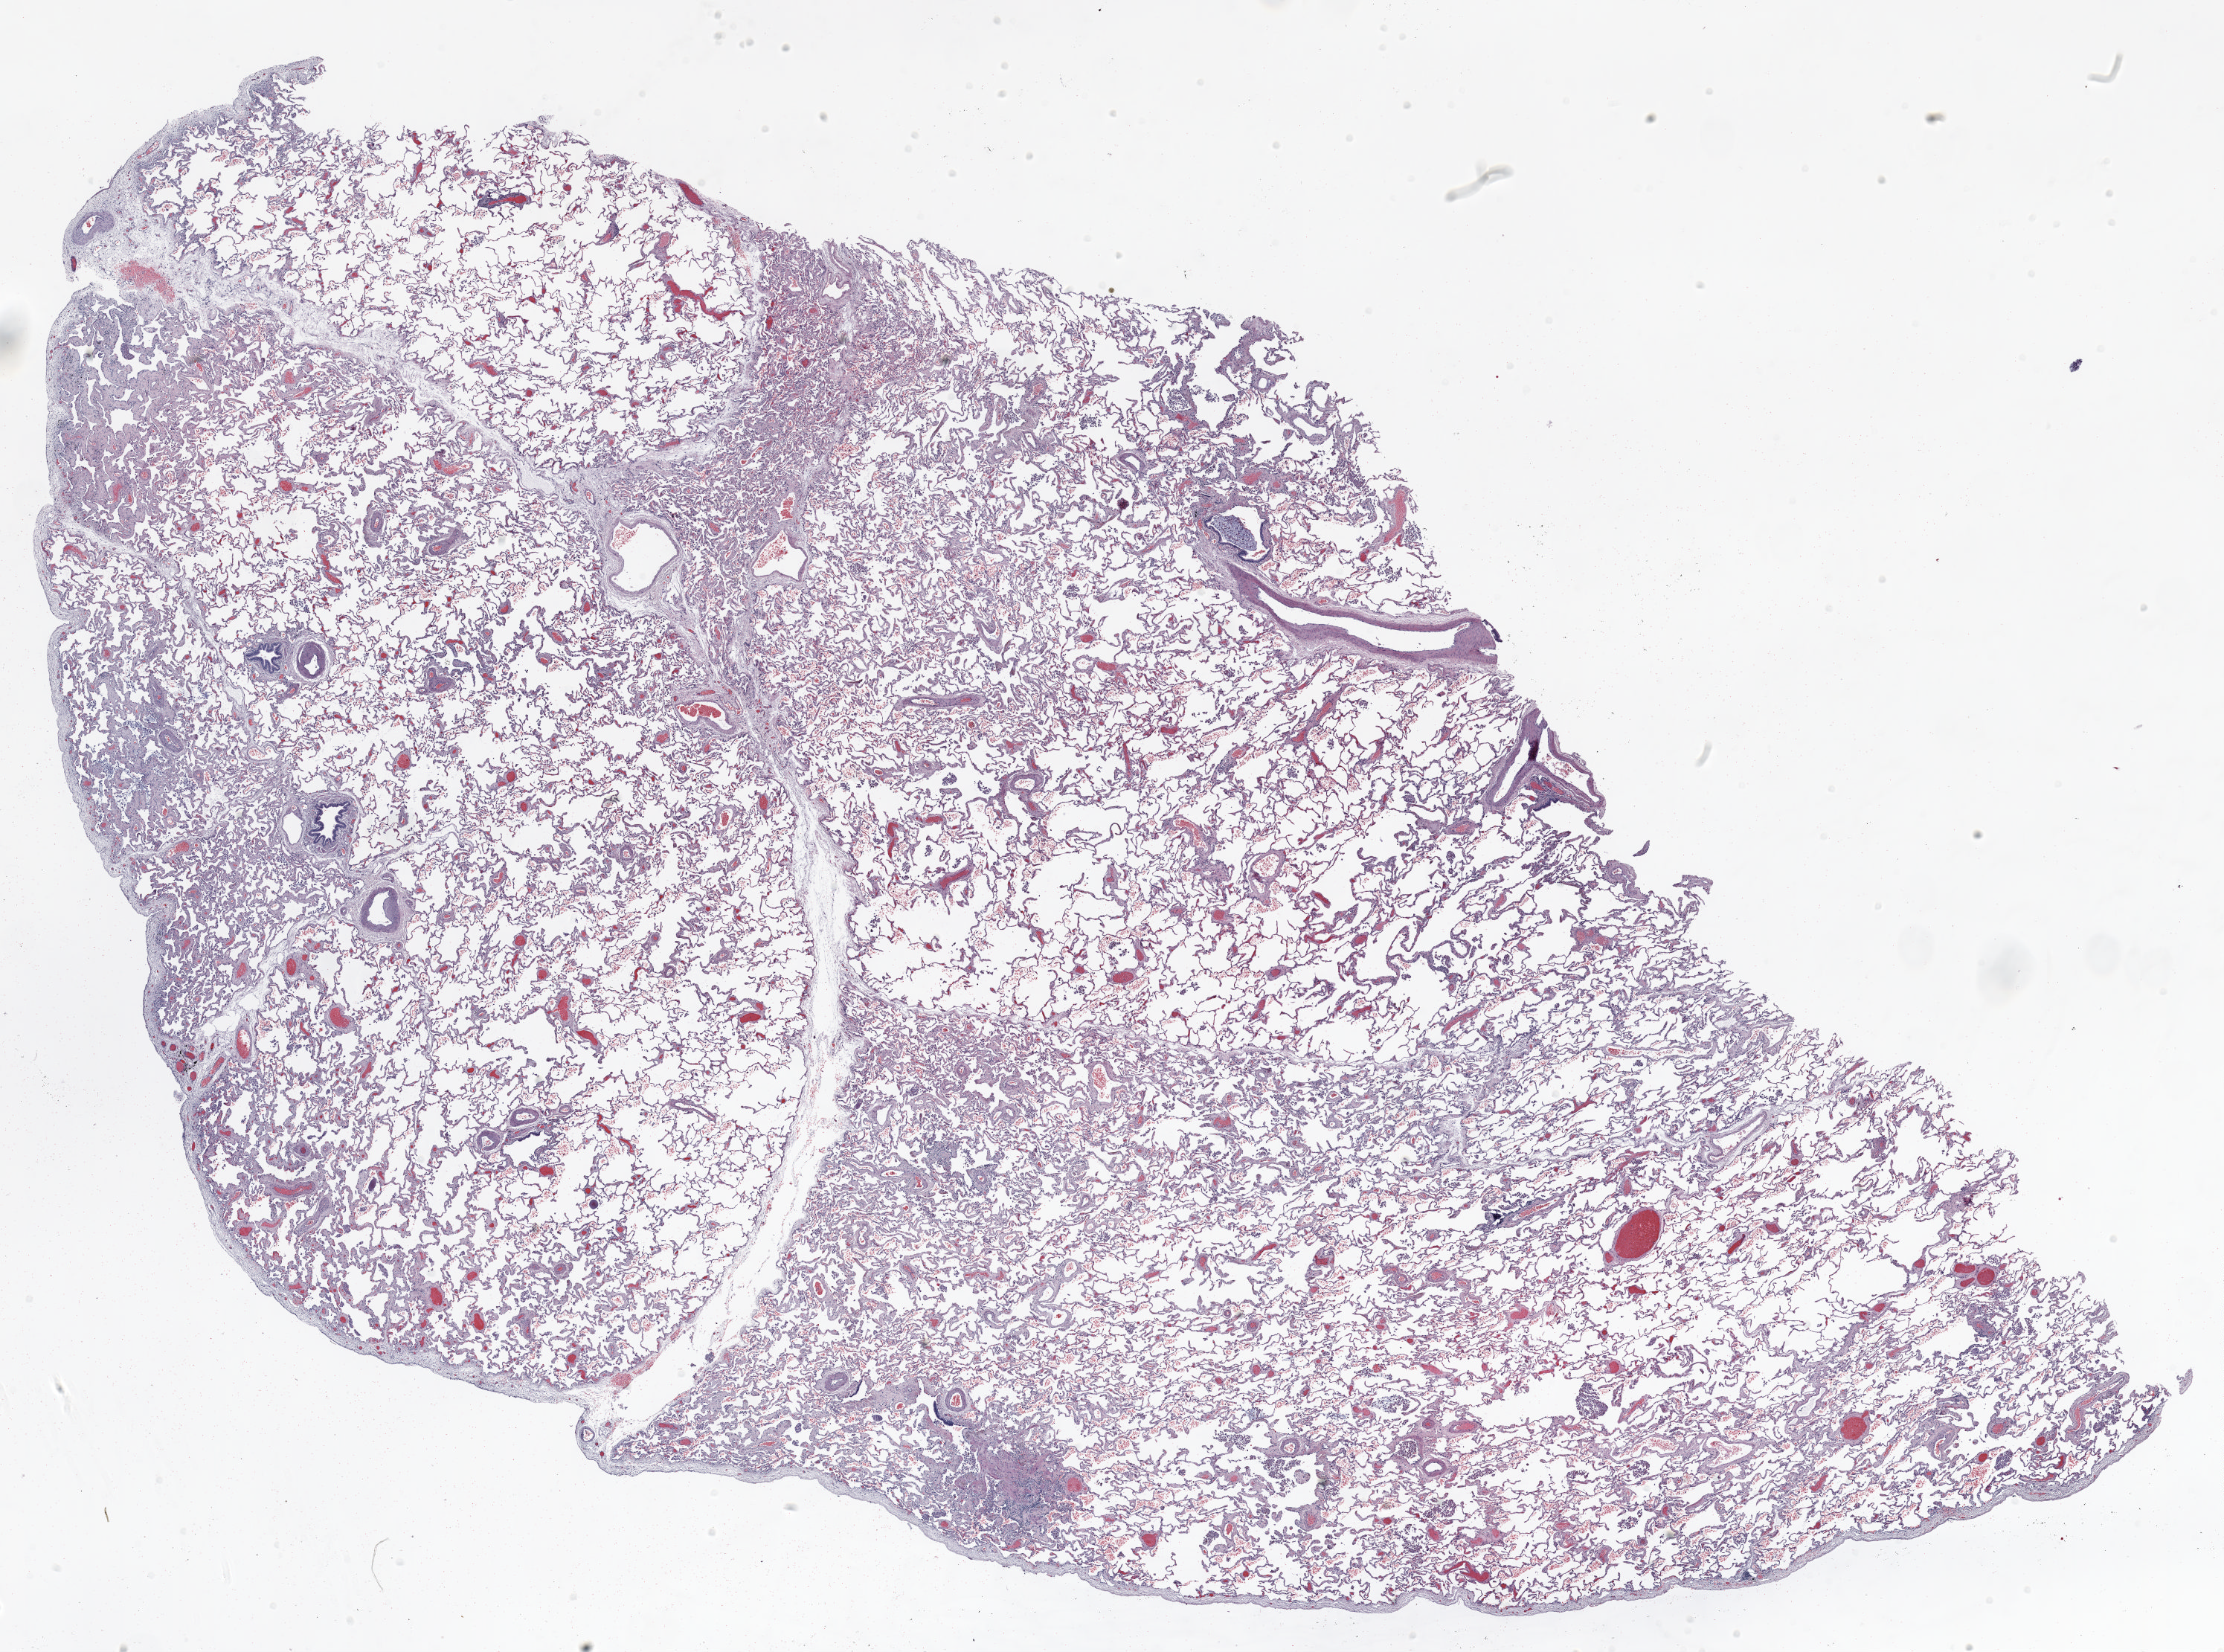
Whole-slide histology image, H&E, a low-resolution overview of the entire scanned area, about 24.0 x 17.8 mm. Formalin-fixed paraffin-embedded (FFPE) section. Lung tissue. Male, age 68 at enrolment. Current smoker at enrolment. Grade: moderately differentiated (G2).
* stage (AJCC 6th edition): IA
* primary tumour location (clinical record): right upper lobe
* participant's lung-cancer diagnosis: Adenocarcinoma, NOS
* tumour size (pathology): 13 mm